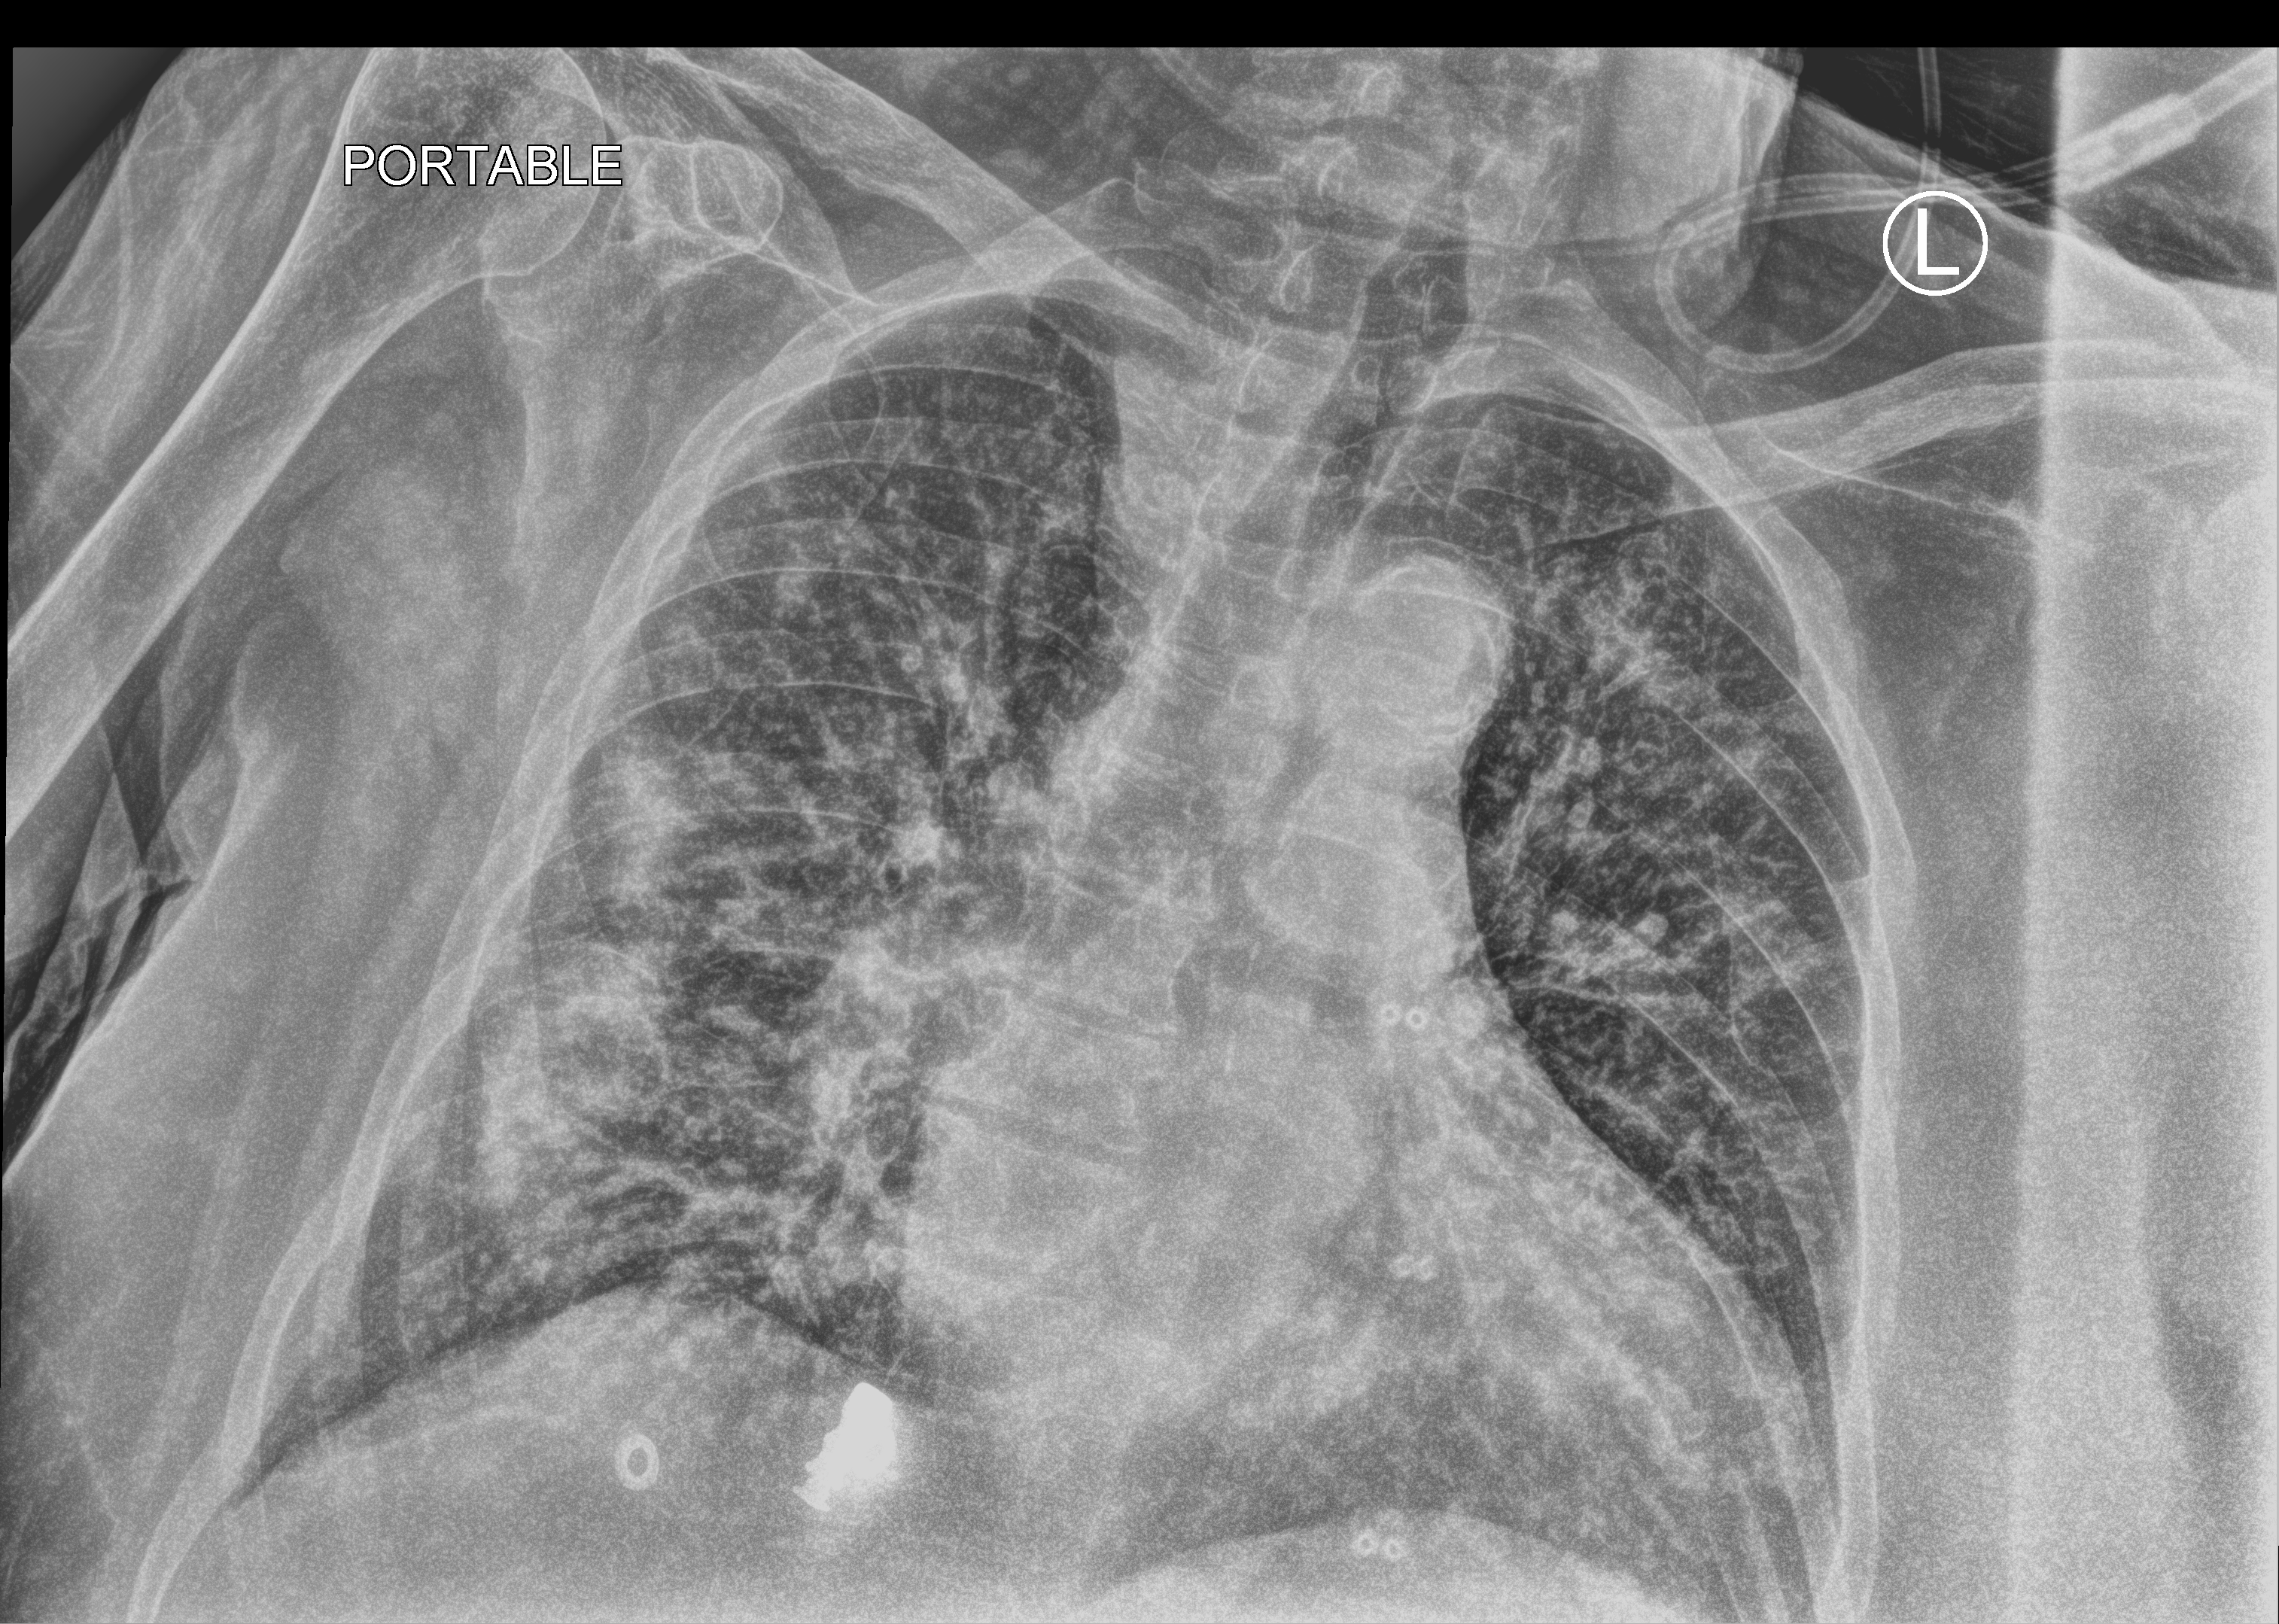
Chest X-ray (portable), anteroposterior (AP) projection. Female patient hospitalised with COVID-19, age 75–90 years.
From the hospital-stay record, not from the radiograph (when in the stay this image was taken is not recorded):
- admitted to intensive care during this hospital stay: no
- mechanically ventilated during this hospital stay: no
- diabetes (admission record): no